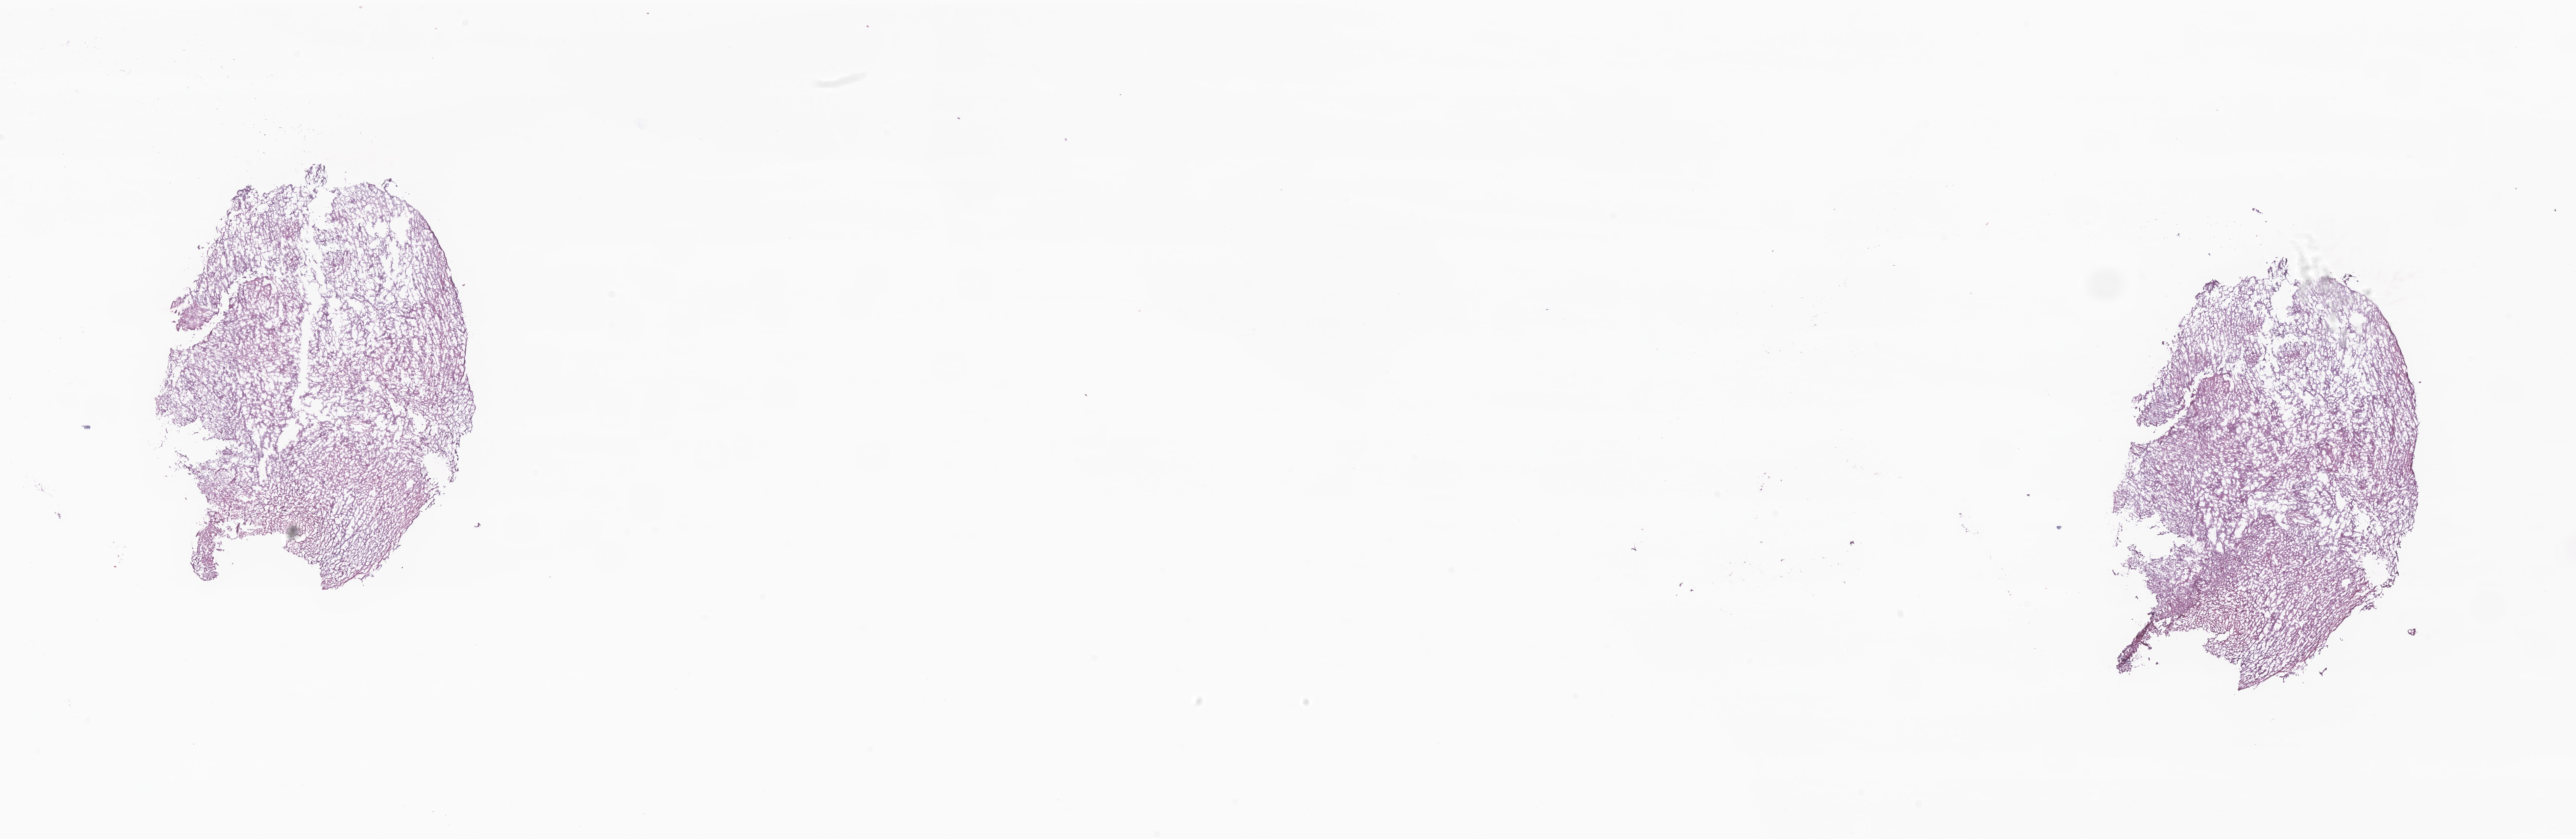
Haematoxylin and eosin whole-slide image of tumor tissue from the brain — whole scanned area (about 32.1 x 10.5 mm) shown as a low-resolution overview. Frozen section (OCT-embedded). Female patient, age 53 months (4 years 5 months).
• diagnosis (ICD-O-3 morphology term): Pilocytic astrocytoma